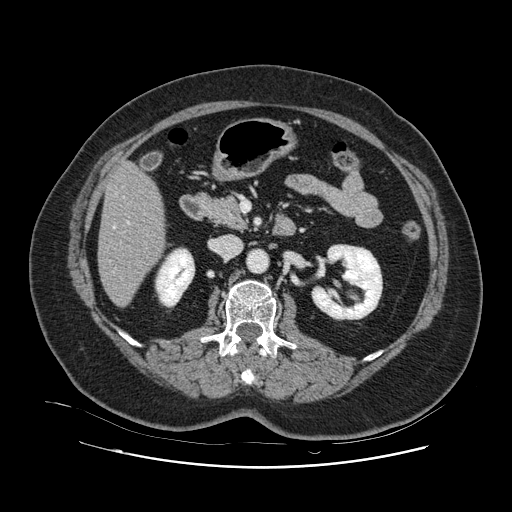
Contrast-enhanced abdominal CT, one axial slice. Slice 37 of 132 in the series (ordered by position). Intravenous contrast given. Soft-tissue window (W 400 / L 40 HU). 2.5 mm slice thickness. 512 × 512 image matrix. Female patient, age 73 years. Case-level facts recorded for this patient, not image findings: diagnosis: colorectal cancer liver metastases, imaged before liver resection; multiple liver metastases: no; largest metastasis: 7 cm; disease in both lobes: no.
Structures marked on this image (expert manual segmentation):
- hepatic veins: bounding box <113,226,116,269> (left, top, right, bottom; pixels)
- liver: <98,164,164,306>
- planned liver remnant (the part of the liver to remain after resection): <98,164,163,306>
- portal vein (with intrahepatic branches): <127,221,130,224>